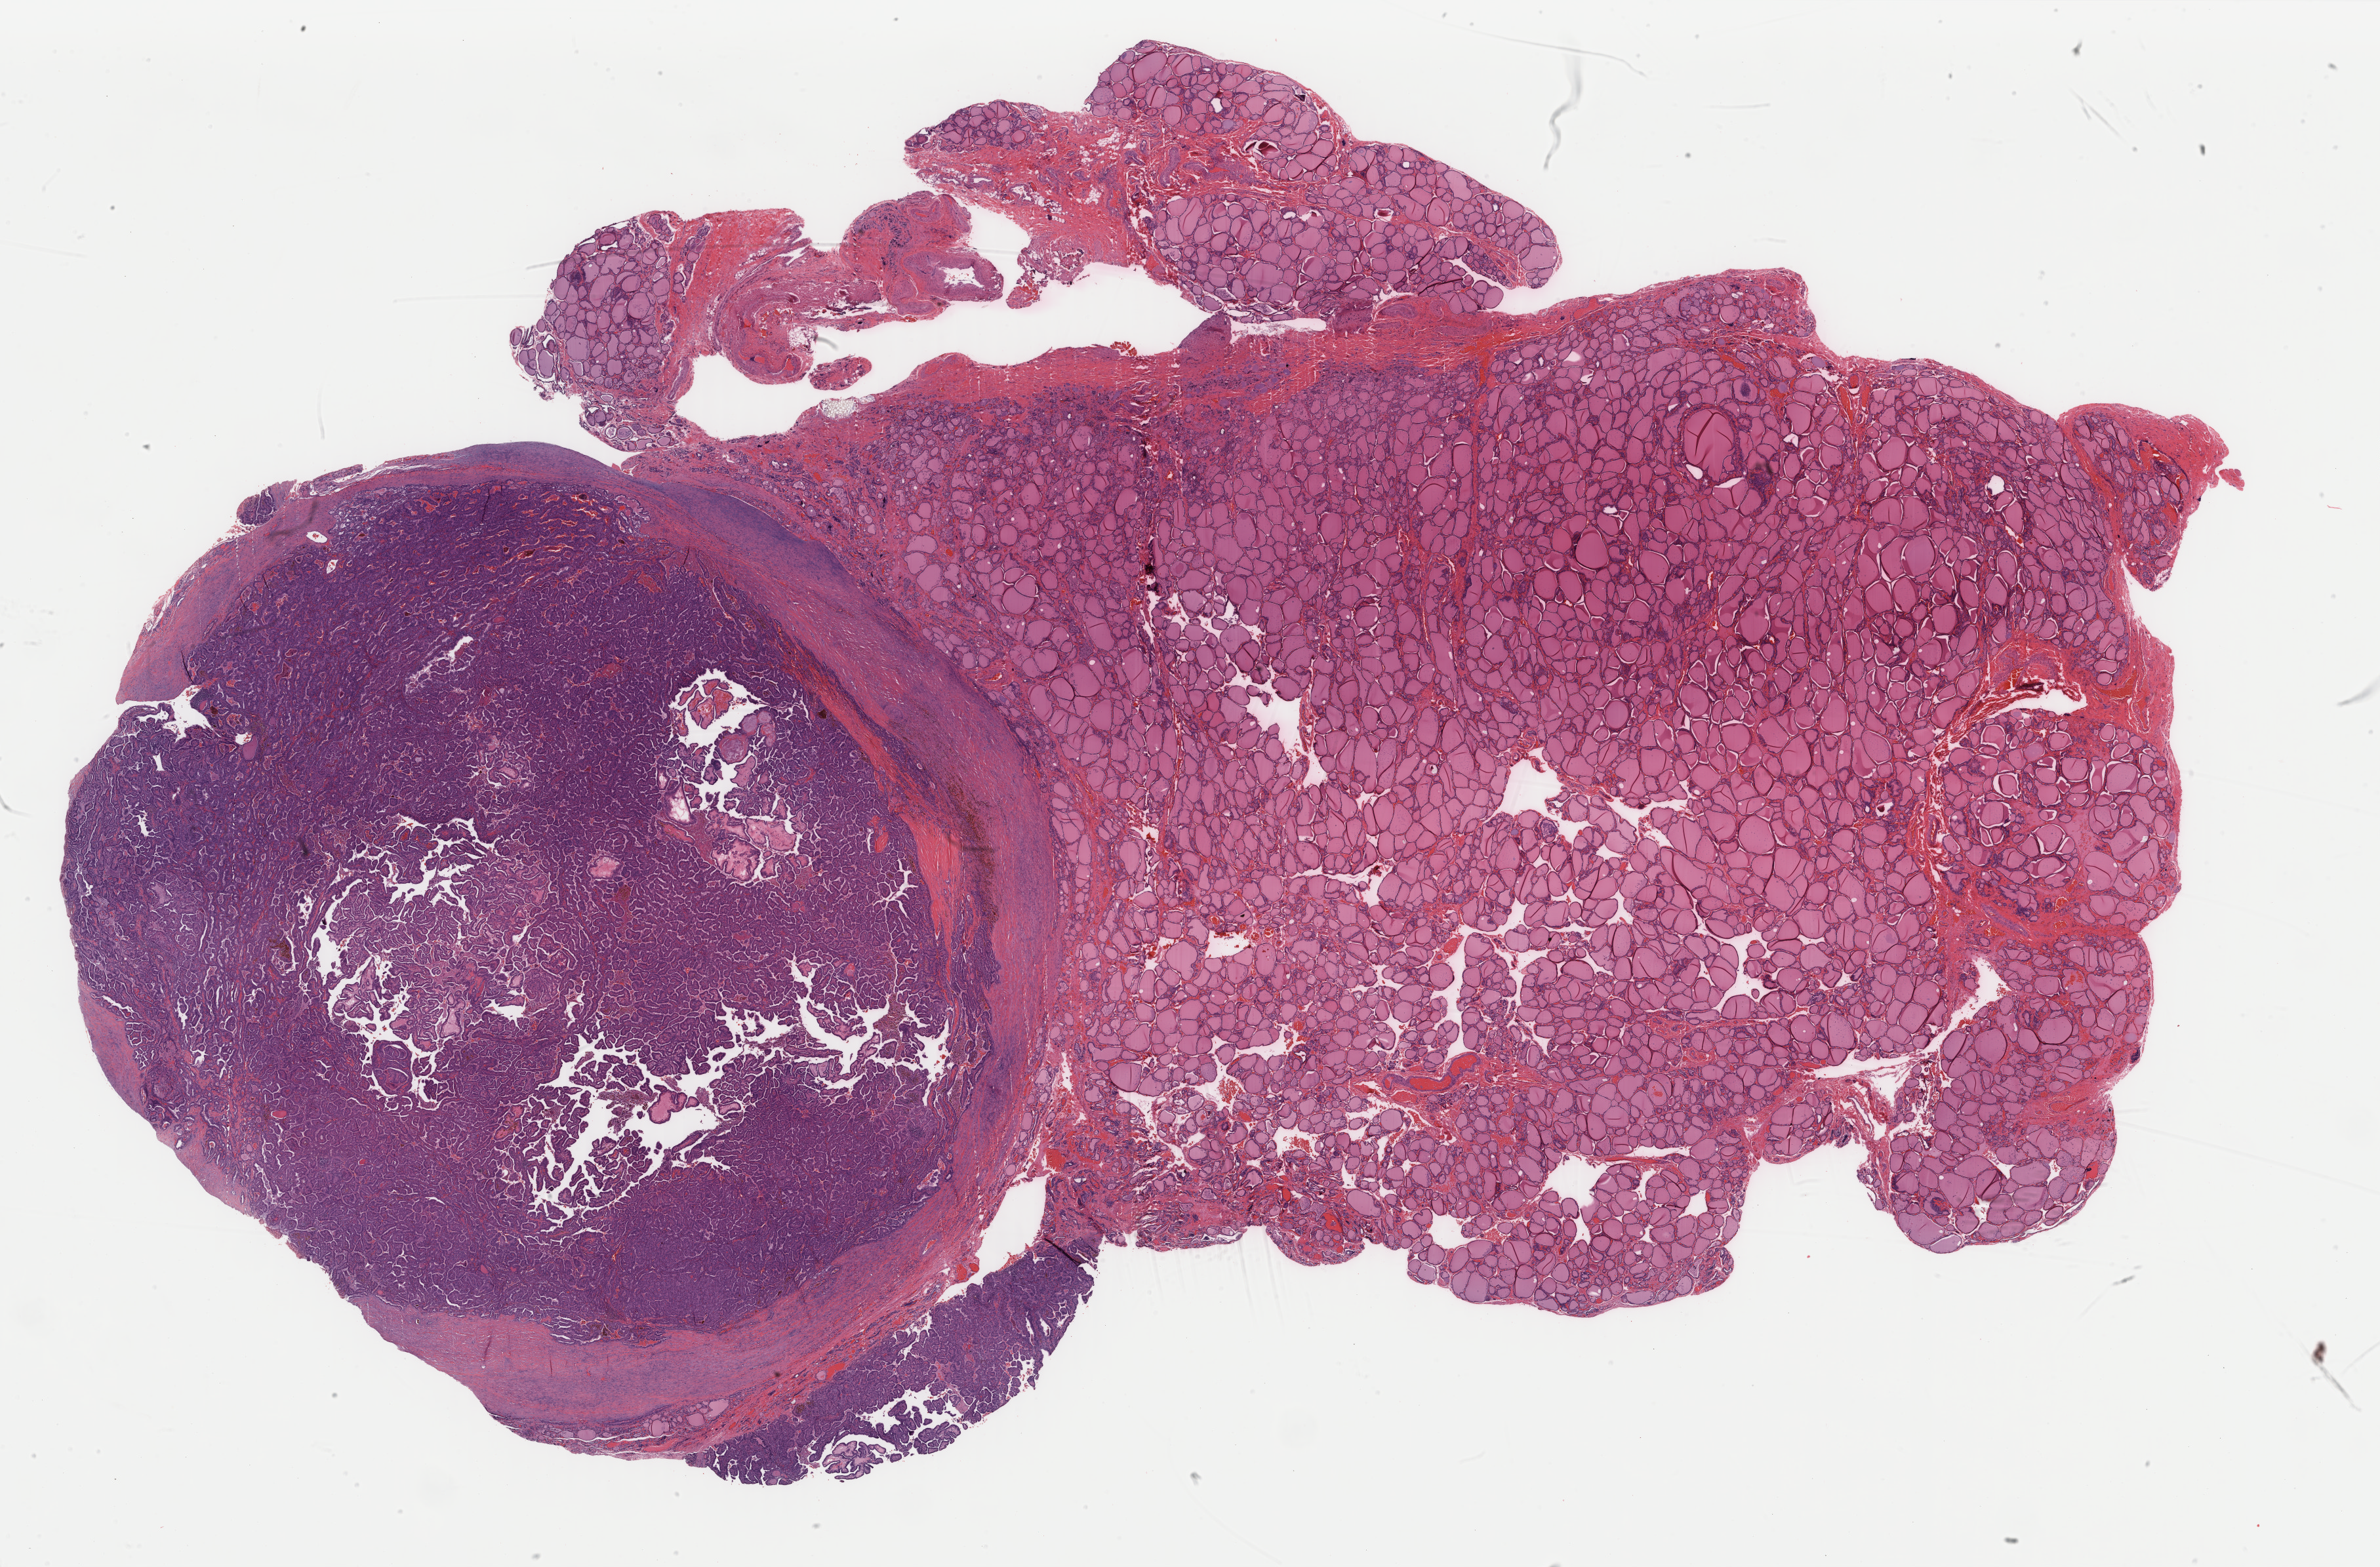
Whole-slide histology image, H&E — a low-resolution overview of the entire scanned area, about 28.8 x 19.0 mm. FFPE section. Sample: primary tumour, thyroid. Female, age 40 years at initial diagnosis.
Diagnosis: Papillary adenocarcinoma, NOS (thyroid gland).